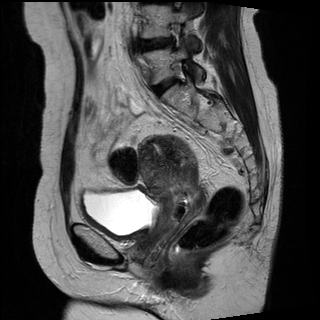
Pelvic MRI for cervical cancer, one sagittal slice. Slice 11 of 27 in the series (ordered by position). T2-weighted. 1.5 T. TE 89 ms, TR 2740 ms. 4 mm slice thickness. 320 × 320 image matrix, field of view 260 × 260 mm. Female patient, age 42 years.
Outlined on this slice (outlined manually by an expert reader):
- uterus and cervix: bounding box [x1, y1, x2, y2] px = [137, 133, 203, 236]